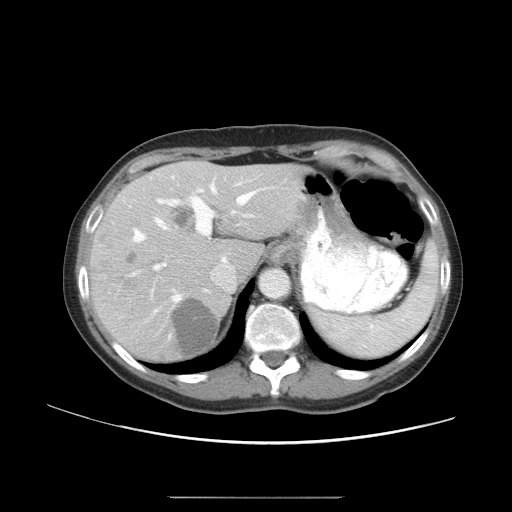
Contrast-enhanced abdominal CT, one axial slice. Position 35 of 50 along the scan axis. 120 kVp. Soft-tissue window (W 400 / L 40 HU). 5 mm slice thickness. 512 × 512 image matrix, field of view 389 × 389 mm. Female patient, age 58 years. Case-level facts recorded for this patient, not image findings: diagnosis: colorectal cancer liver metastases, imaged before liver resection; multiple liver metastases: yes; largest metastasis: 7.3 cm; disease in both lobes: yes.
Outlined on this slice (manually delineated by an expert):
- hepatic veins: bounding box <134,178,266,313> (left, top, right, bottom; pixels)
- liver: <95,161,299,359>
- planned liver remnant (the part of the liver to remain after resection): <172,161,299,274>
- portal vein (with intrahepatic branches): <154,180,255,270>
- liver metastasis: <172,300,219,353>
- liver metastasis: <174,210,194,229>